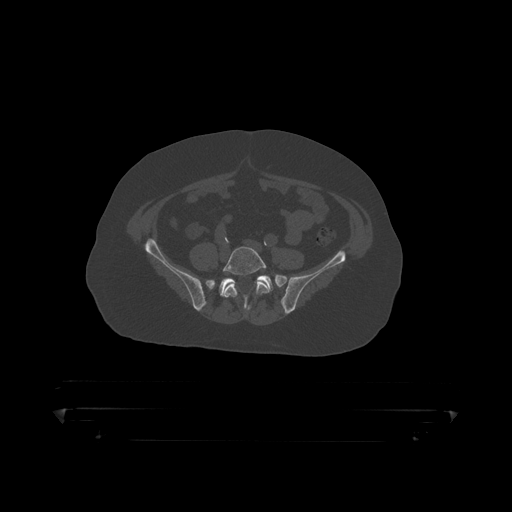
CT including the spine, one axial slice; reconstruction kernel STANDARD; 120 kVp; bone window (W 1800 / L 400 HU); 512 × 512 image matrix, field of view 650 × 650 mm. Patient: male, 60 years. Case-level facts recorded for this patient, not image findings: primary cancer: prostate.
Annotated regions visible in this slice (semi-automatically segmented with operator editing):
- L5 vertebra: bounding box [x1, y1, x2, y2] px = [222, 246, 273, 312]